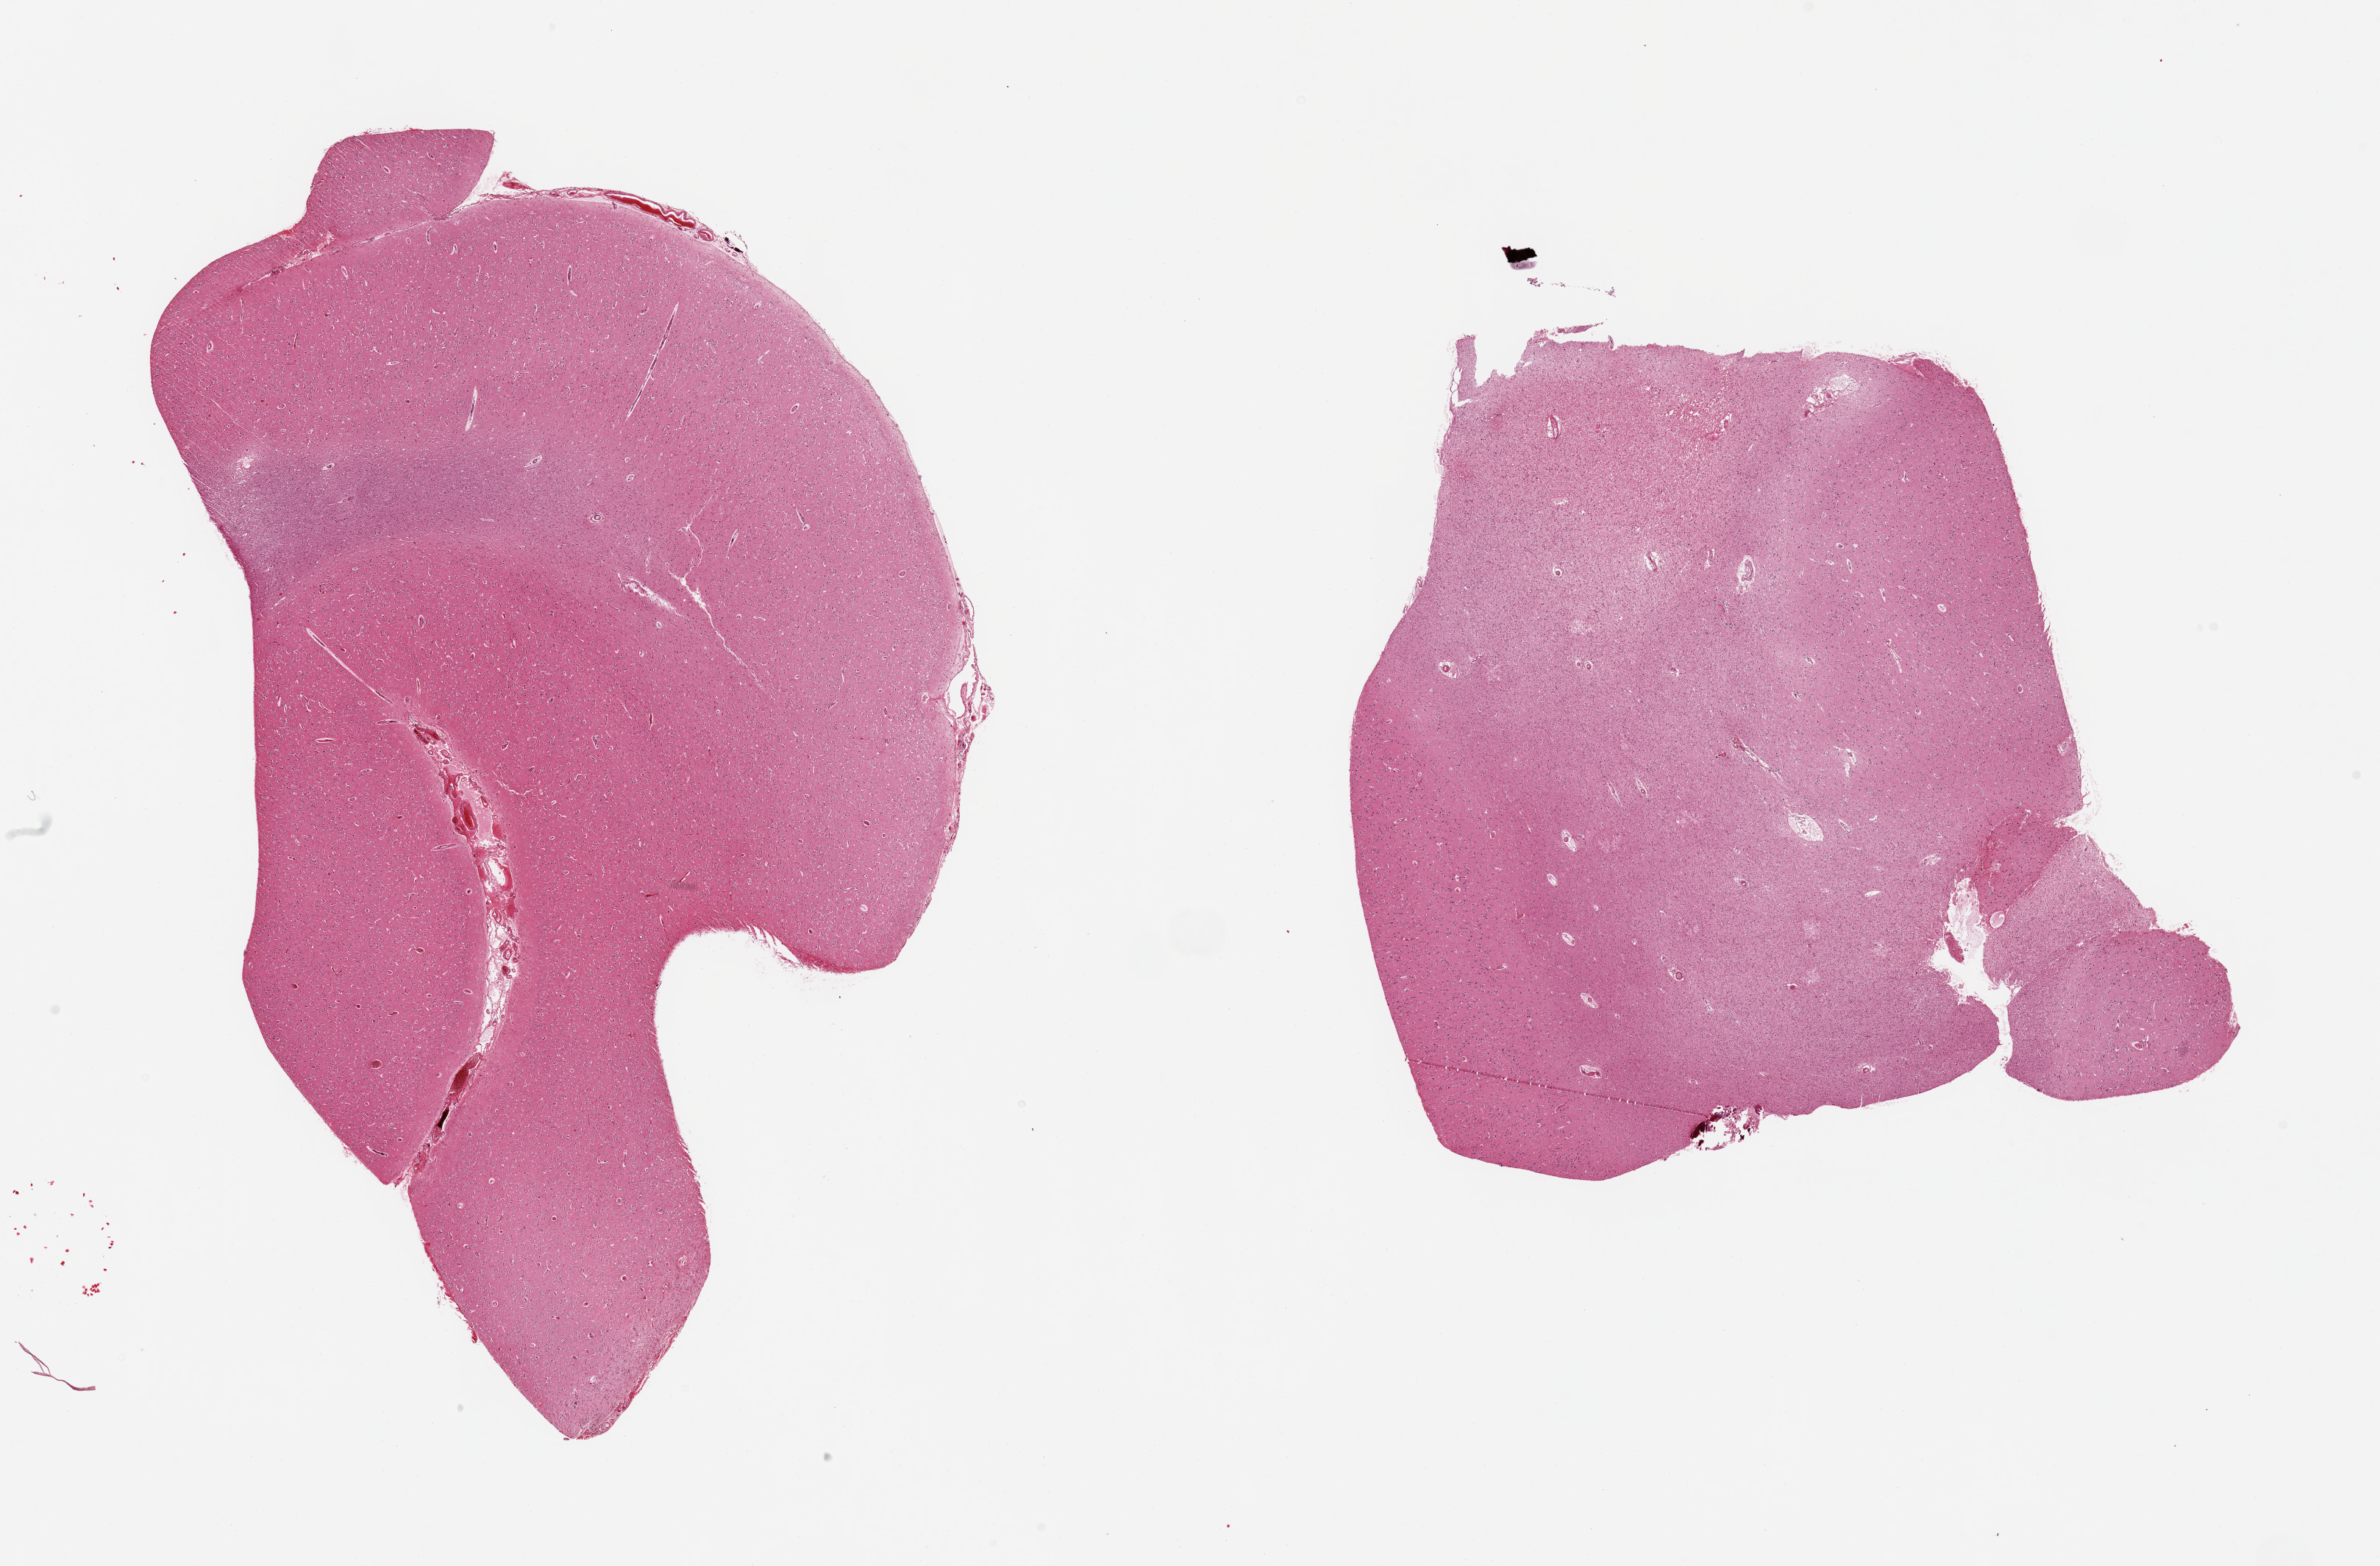
Digitized H&E-stained section — low-resolution overview of the scanned area, about 25.6 x 16.8 mm, PAXgene-fixed paraffin-embedded (PFPE) section, section of cerebral cortex (target tissue), tissue donor sample. Donor: female.
Pathologist's review note for this sample: 2 pieces, no abnormalties.